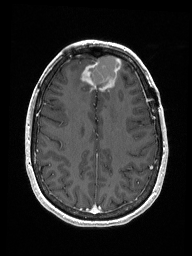
Brain MRI from a brain-tumour surgery series, one axial slice. T1-weighted post-contrast. 192 × 256 image matrix, field of view 187 × 250 mm. From the clinical record (not read from this slice): histopathology: Metastastic Carcinoma from Breast primary.
Outlined on this slice (expert manual segmentation):
- previous resection cavity: bounding box (x1, y1, x2, y2) in pixels: (90, 56, 119, 87)